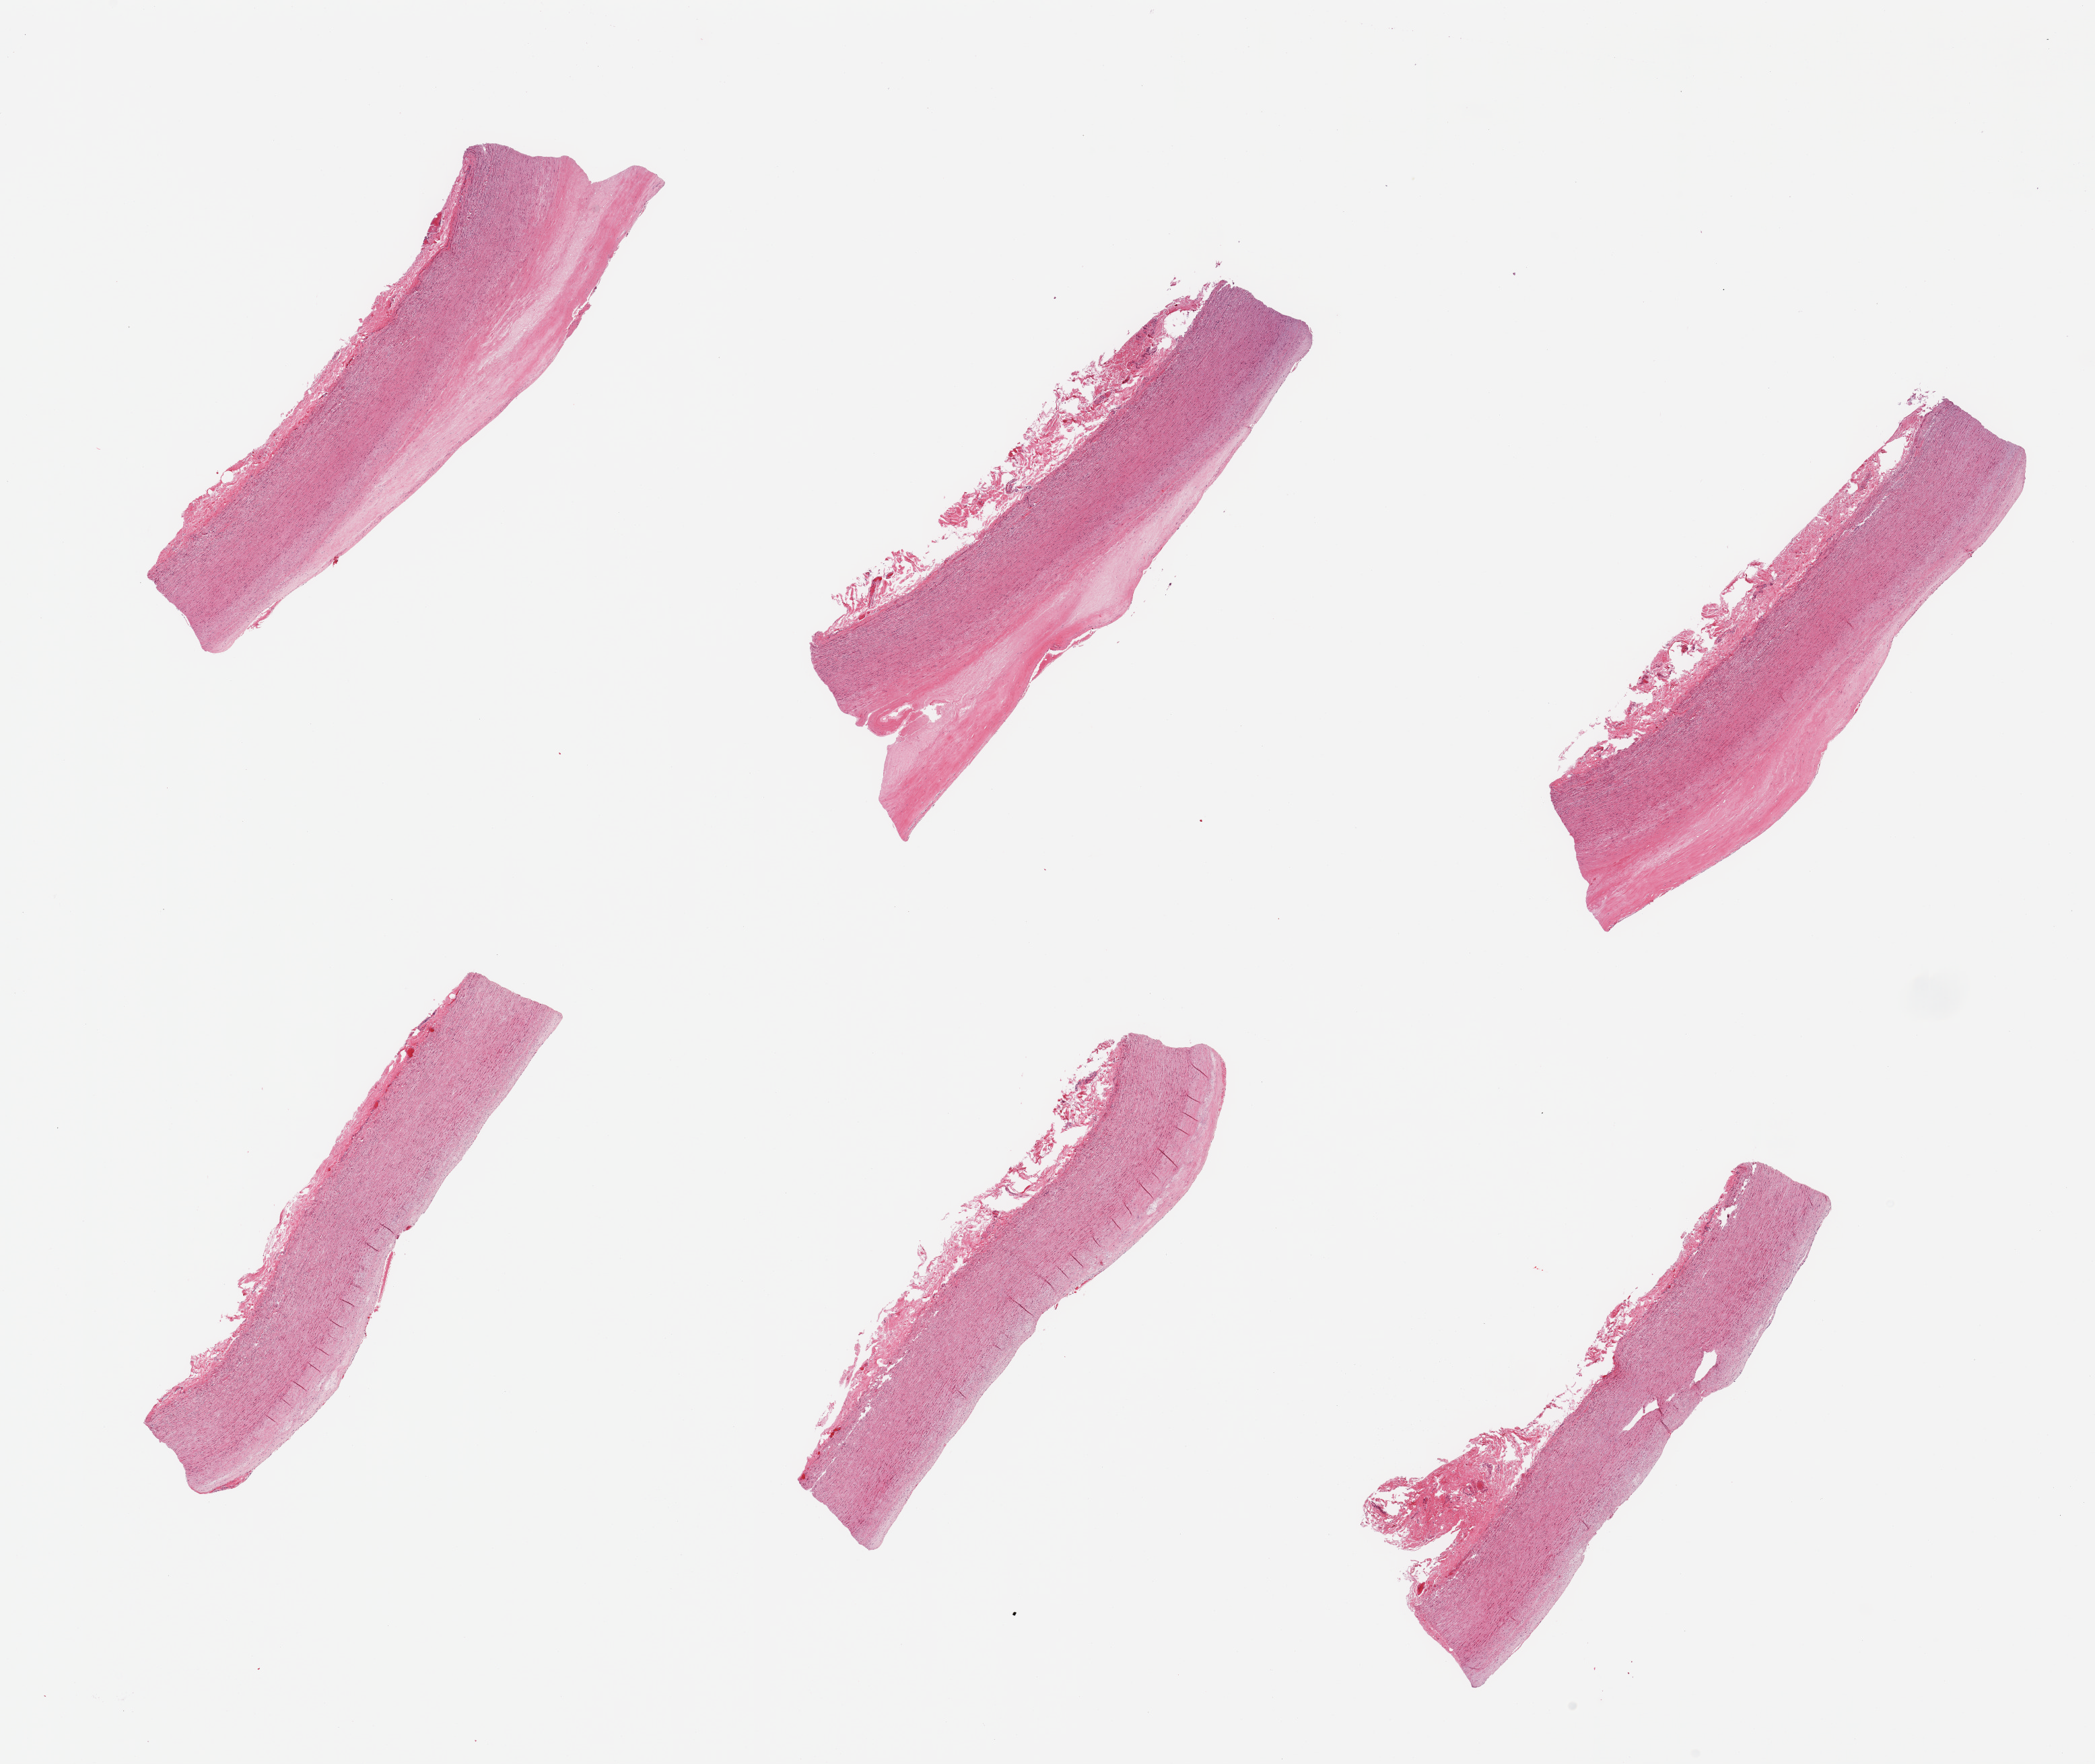
Digitized H&E-stained section, shown as a low-resolution overview of the whole scanned area (about 24.6 x 20.7 mm), PAXgene-fixed paraffin-embedded (PFPE) section, section of aorta (target tissue), donor tissue sample. Donor sex: female.
Pathologist's review note for this sample: 6 pieces; intimal sclerotic plaques up to 0.8mm thick.